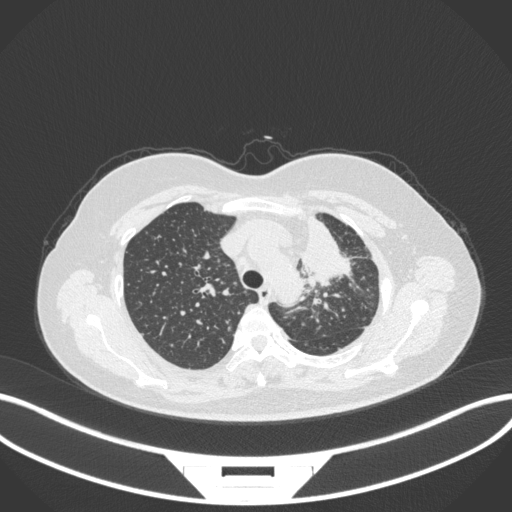
Chest CT, one axial slice; slice 256 of 348 in the series (ordered by position); 120 kVp; lung window (W 1500 / L -600 HU); 1 mm slice thickness; 512 × 512 image matrix. Female patient, age 49 years. Case-level facts recorded for this patient, not image findings: clinical TNM (as recorded): T1c N0 M1.
Outlined on this slice (bounding box drawn by a radiologist):
- lung tumour (recorded histology: adenocarcinoma): bounding box [x1, y1, x2, y2] px = [295, 211, 355, 289]